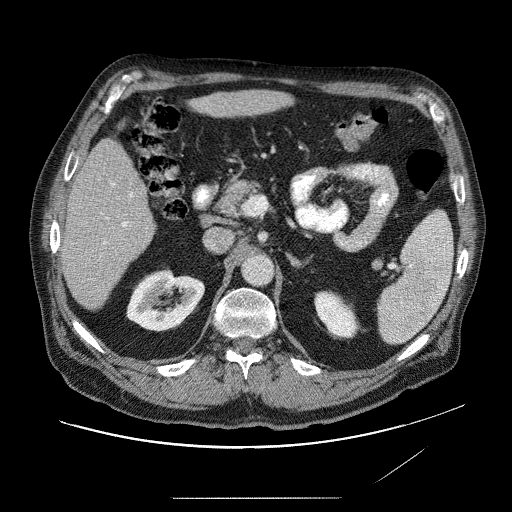
Contrast-enhanced abdominal CT (liver protocol), one axial slice; position 32 of 89 along the scan axis; reconstruction kernel STANDARD; 120 kVp; soft-tissue window (W 400 / L 40 HU); 512 × 512 image matrix, field of view 420 × 420 mm. Case-level facts recorded for this patient, not image findings: diagnosis: hepatocellular carcinoma (patient treated with transarterial chemoembolisation; whether this scan precedes or follows treatment is not stated here); TNM stage (as recorded): Stage-IVA; Child-Pugh class: A; tumour differentiation: moderately differentiated.
Outlined on this slice (semi-automatically segmented with operator editing):
- liver parenchyma outside the tumour (the mass and vessels are separate outlines, so this box may not span the whole liver): box from (x=62, y=86) to (x=302, y=312) px
- mass: (x=187, y=90)–(x=281, y=118)
- liver vessels: (x=101, y=102)–(x=232, y=284)